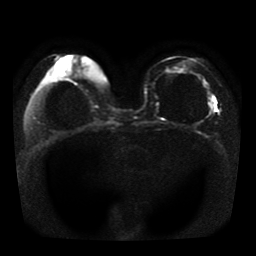
Breast MRI, one axial slice. Diffusion-weighted series; image 2 of 4 stored at this slice position (different b-values; order by instance number). 1.5 T. 256 × 256 image matrix. Female patient.
Structures marked on this image (manually delineated by an expert):
- tumour on diffusion-weighted imaging: box from (x=209, y=102) to (x=214, y=113) px